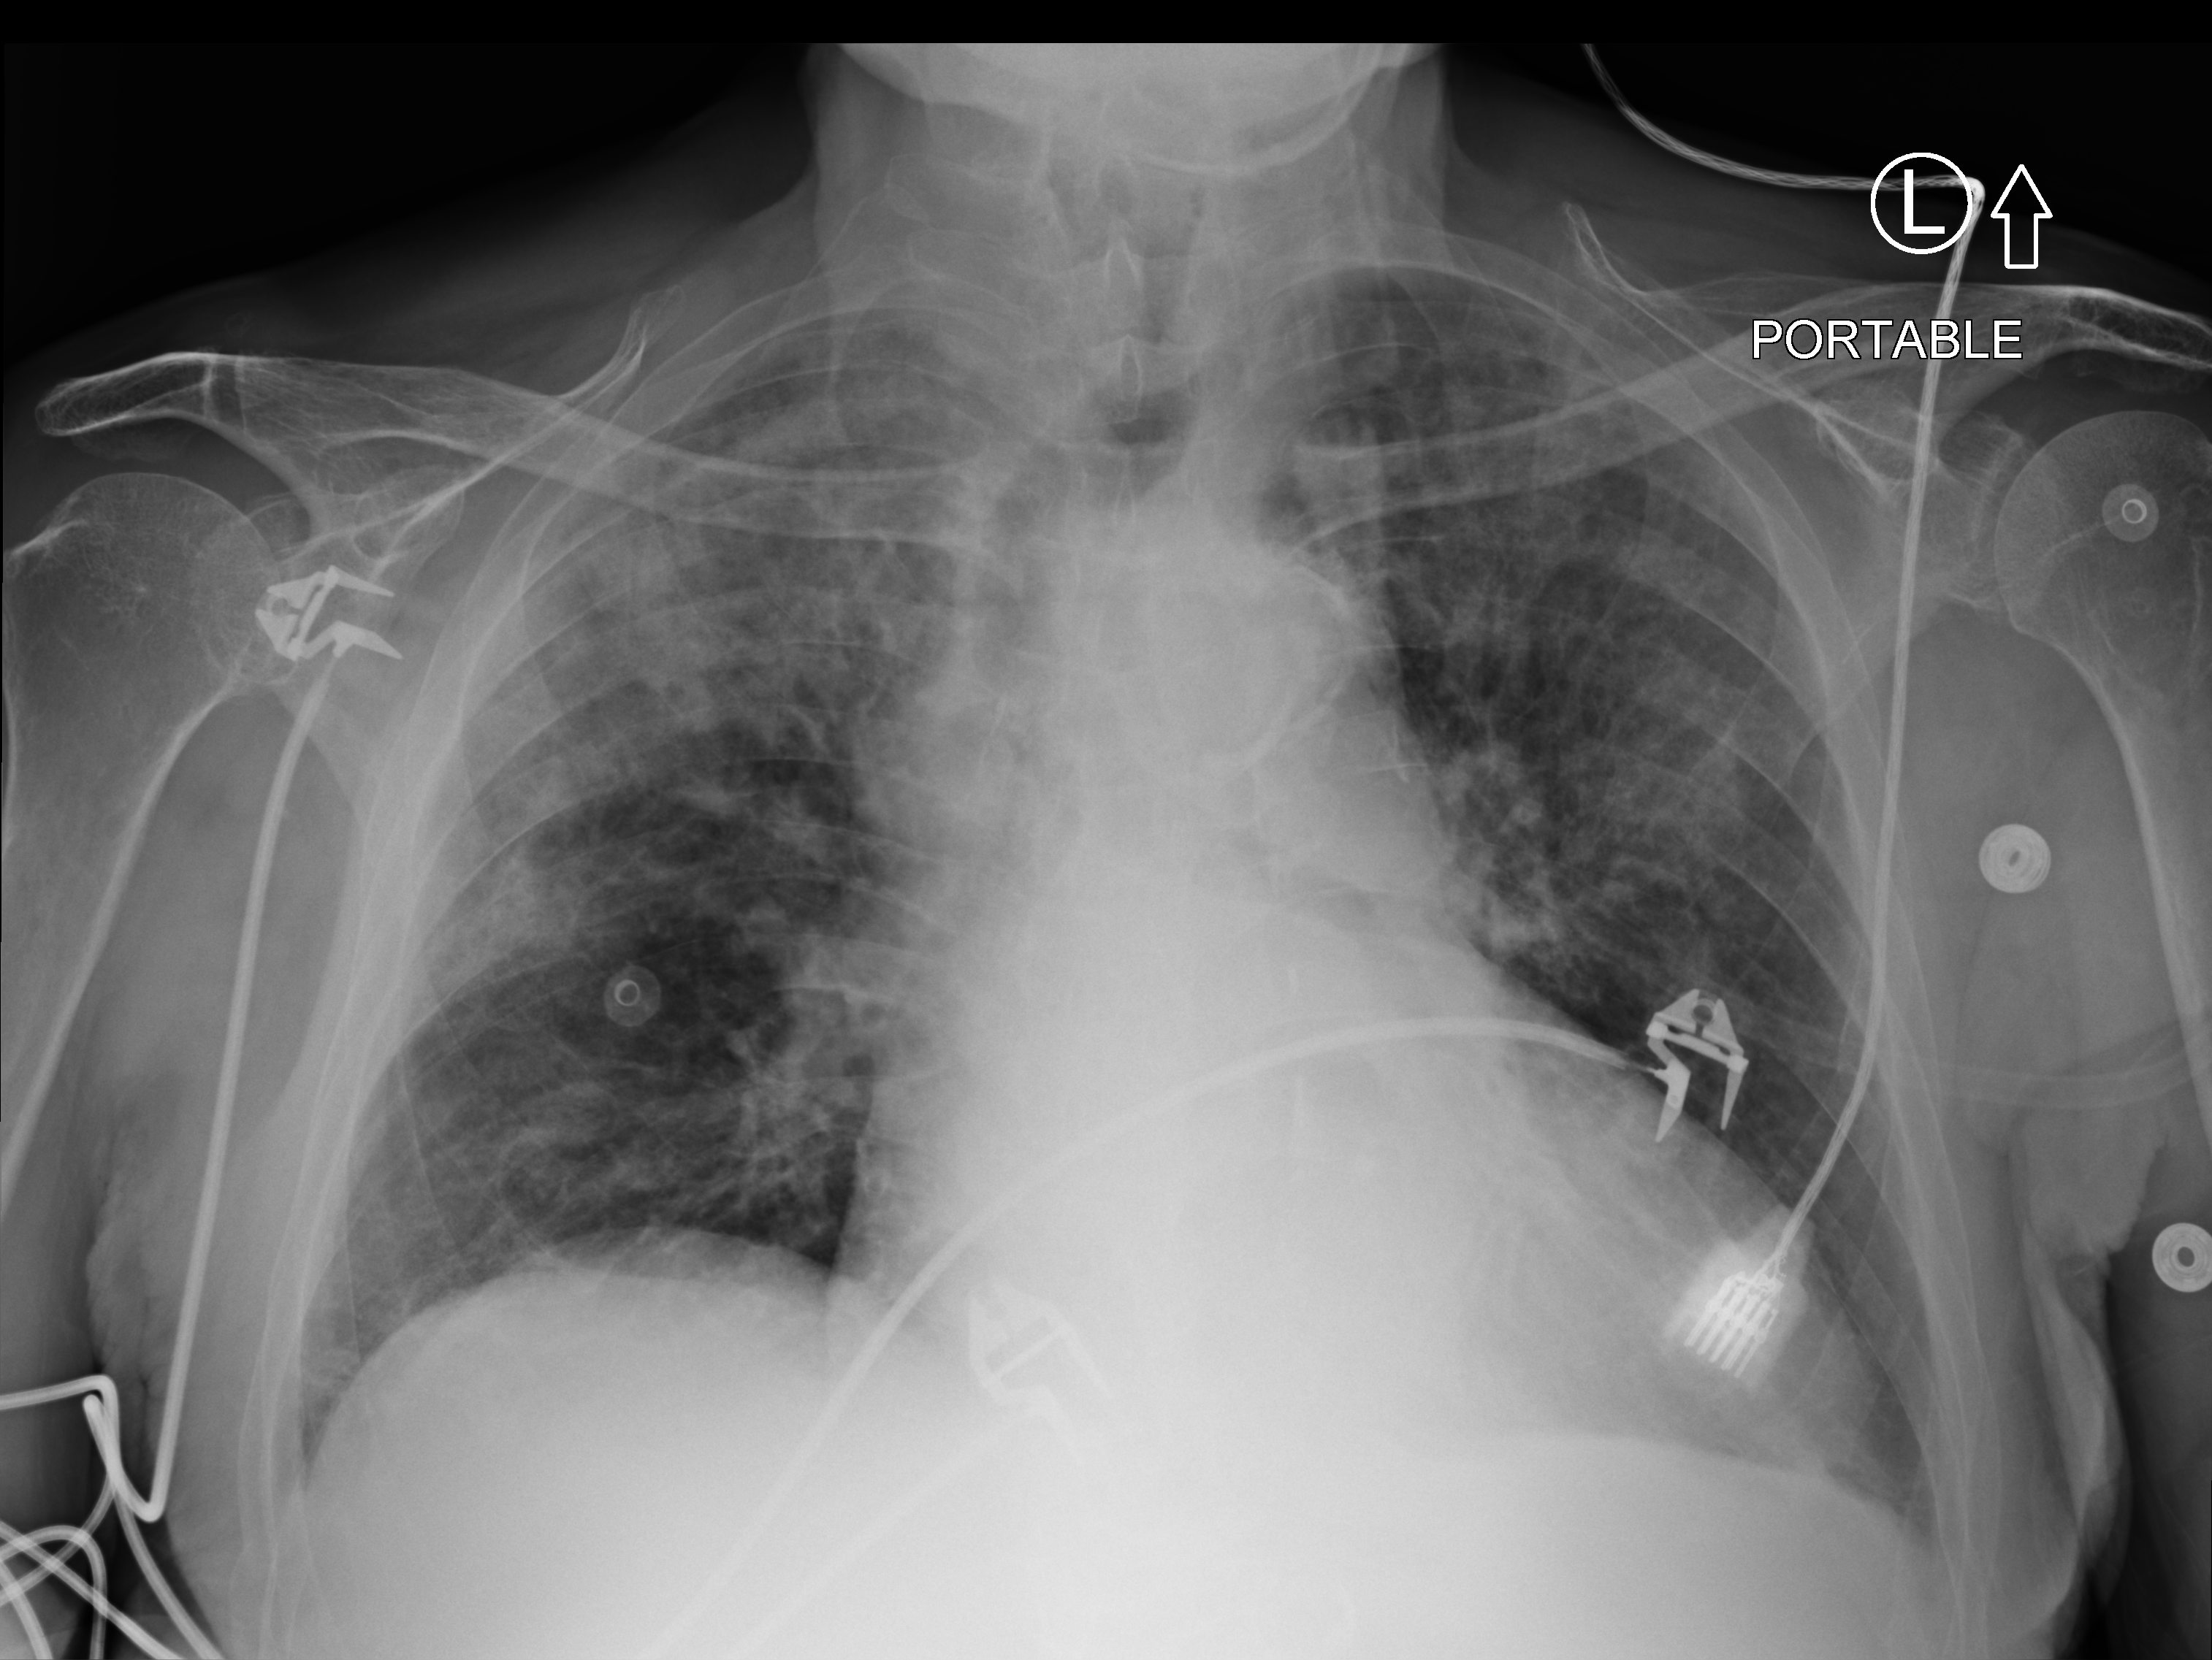
Portable chest radiograph; anteroposterior (AP) projection. Patient hospitalised with COVID-19; male, aged 75–90 years.
Admission-level facts for this patient (not findings on this image; timing relative to this image not recorded): admitted to intensive care during this hospital stay: no; COPD (admission record): no; mechanically ventilated during this hospital stay: no.